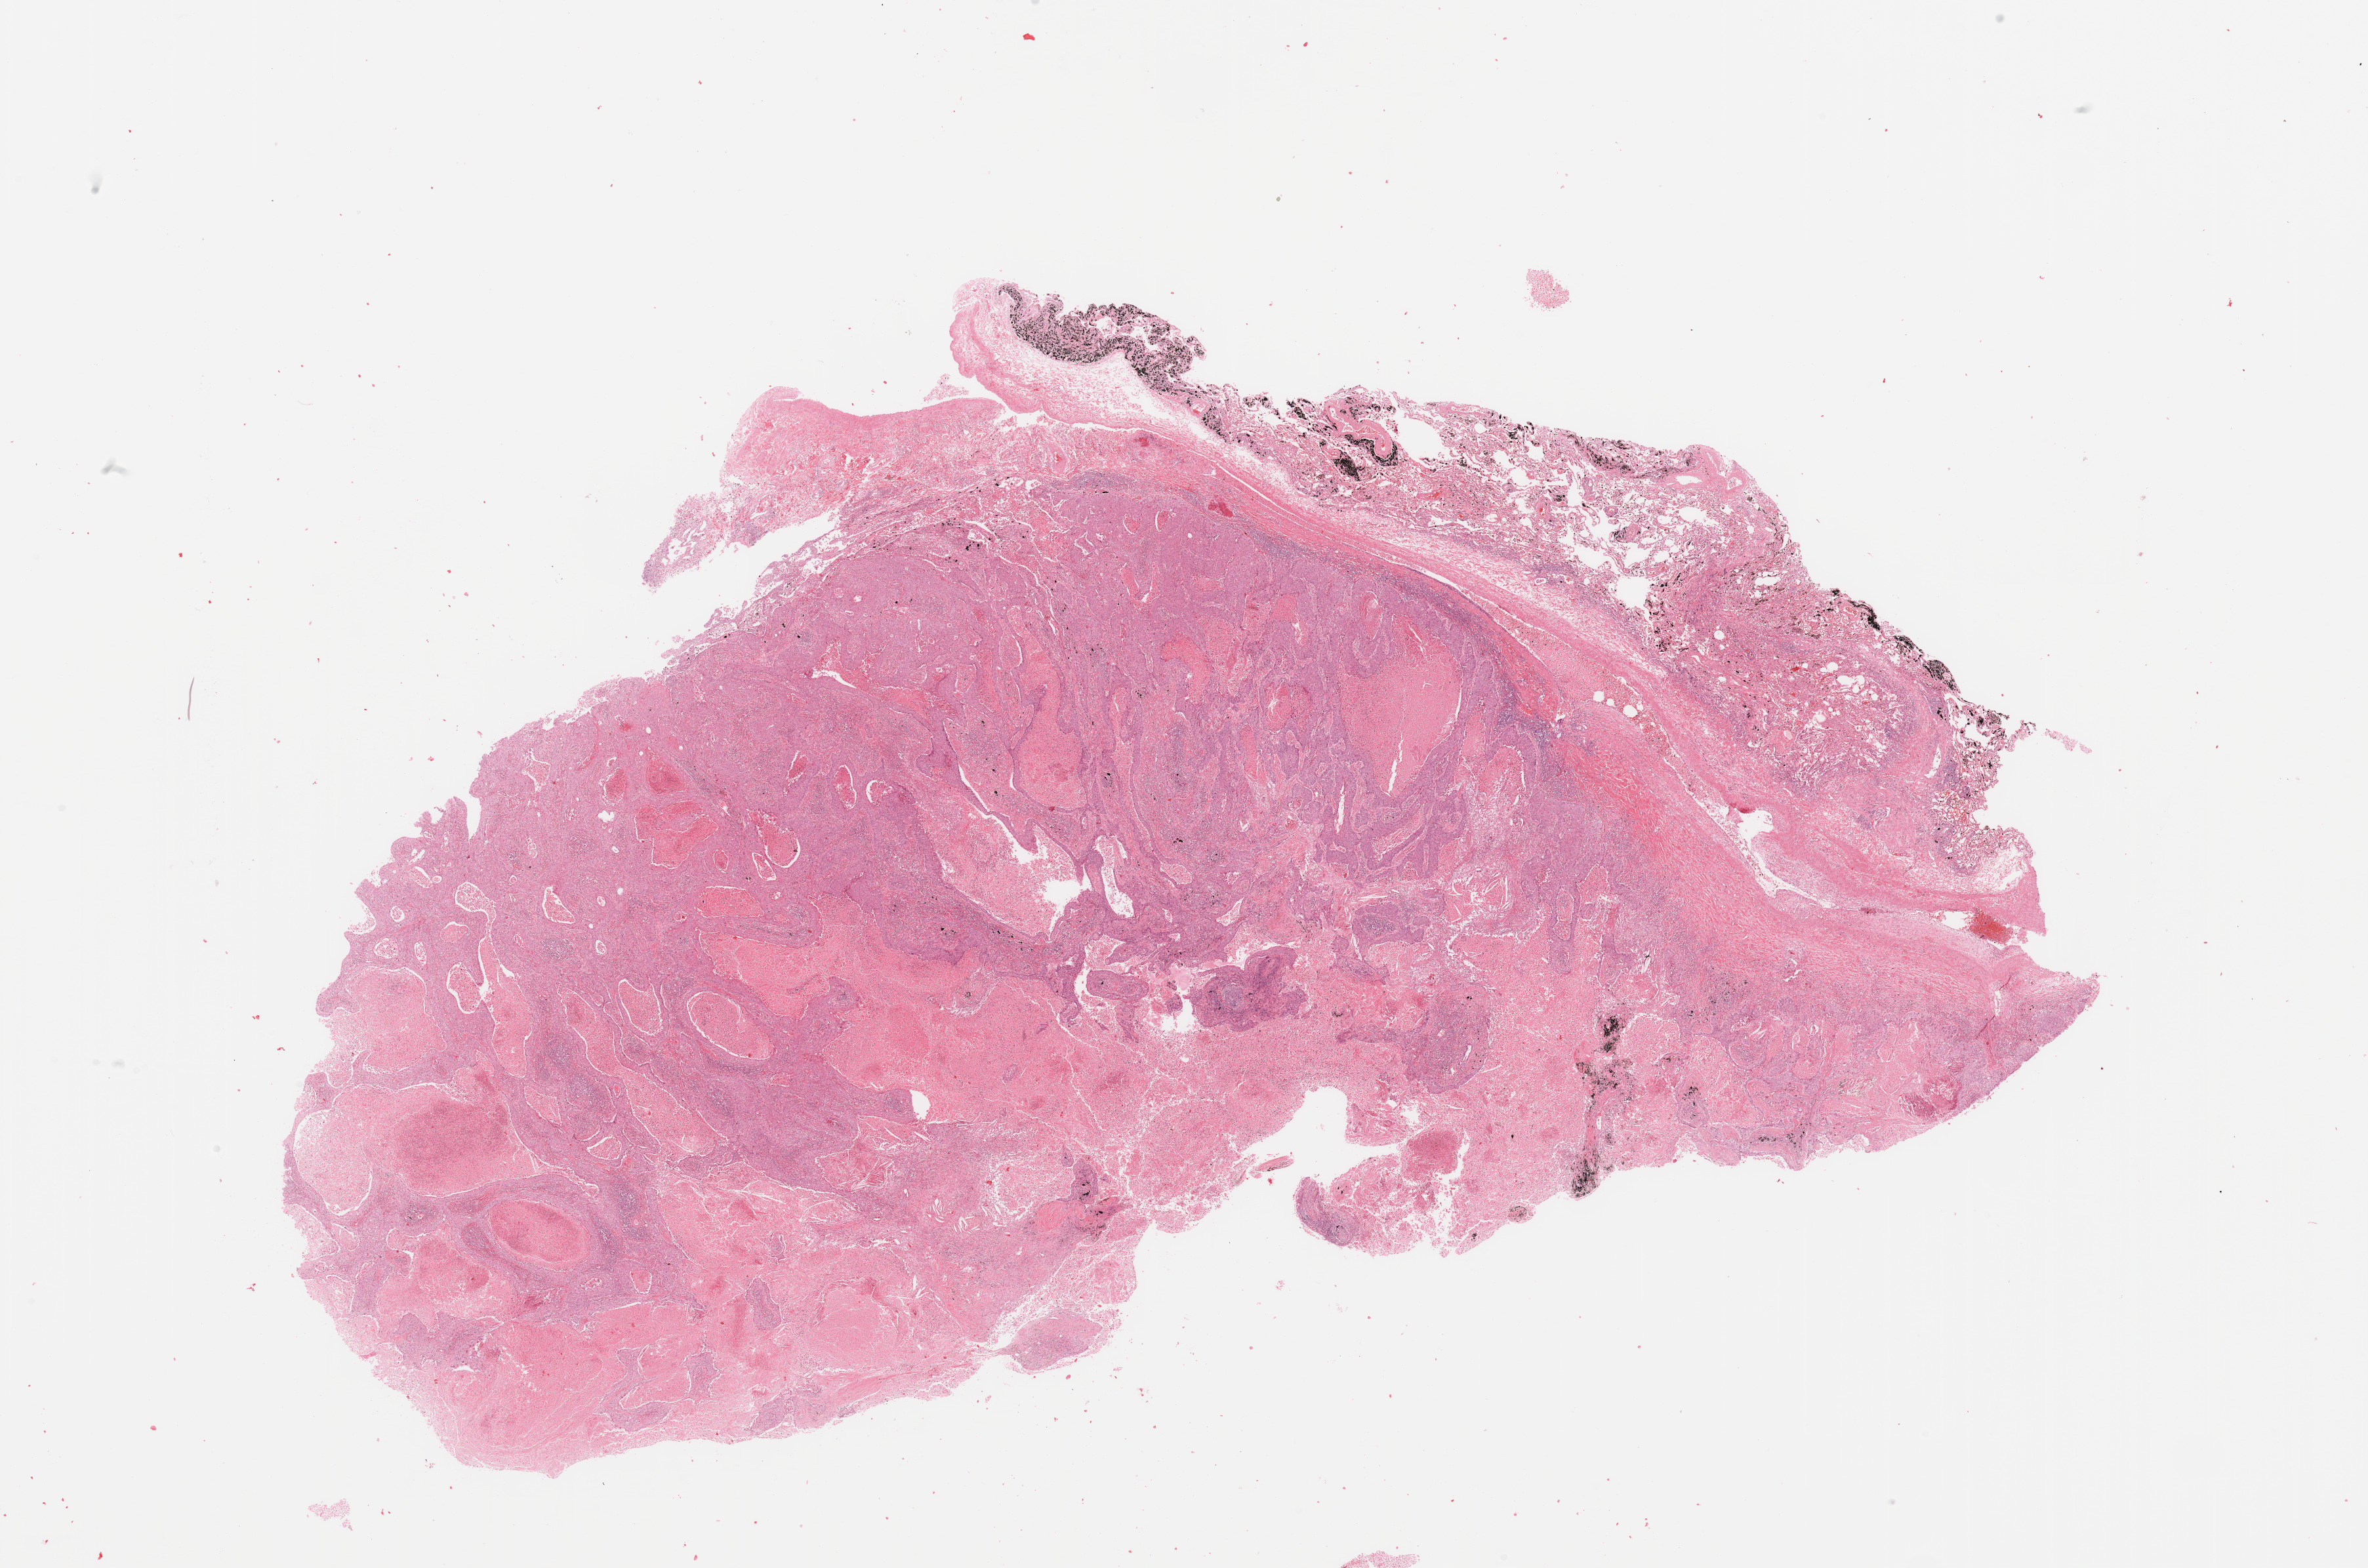
Whole-slide histology image, H&E-stained — a low-resolution overview of the entire scanned area, about 28.5 x 18.9 mm. Lung, tumour tissue. 56-year-old male patient. Histologic grade: G2 (moderately differentiated).
AJCC pathologic stage: IIB. Diagnosis: Squamous cell carcinoma, NOS.